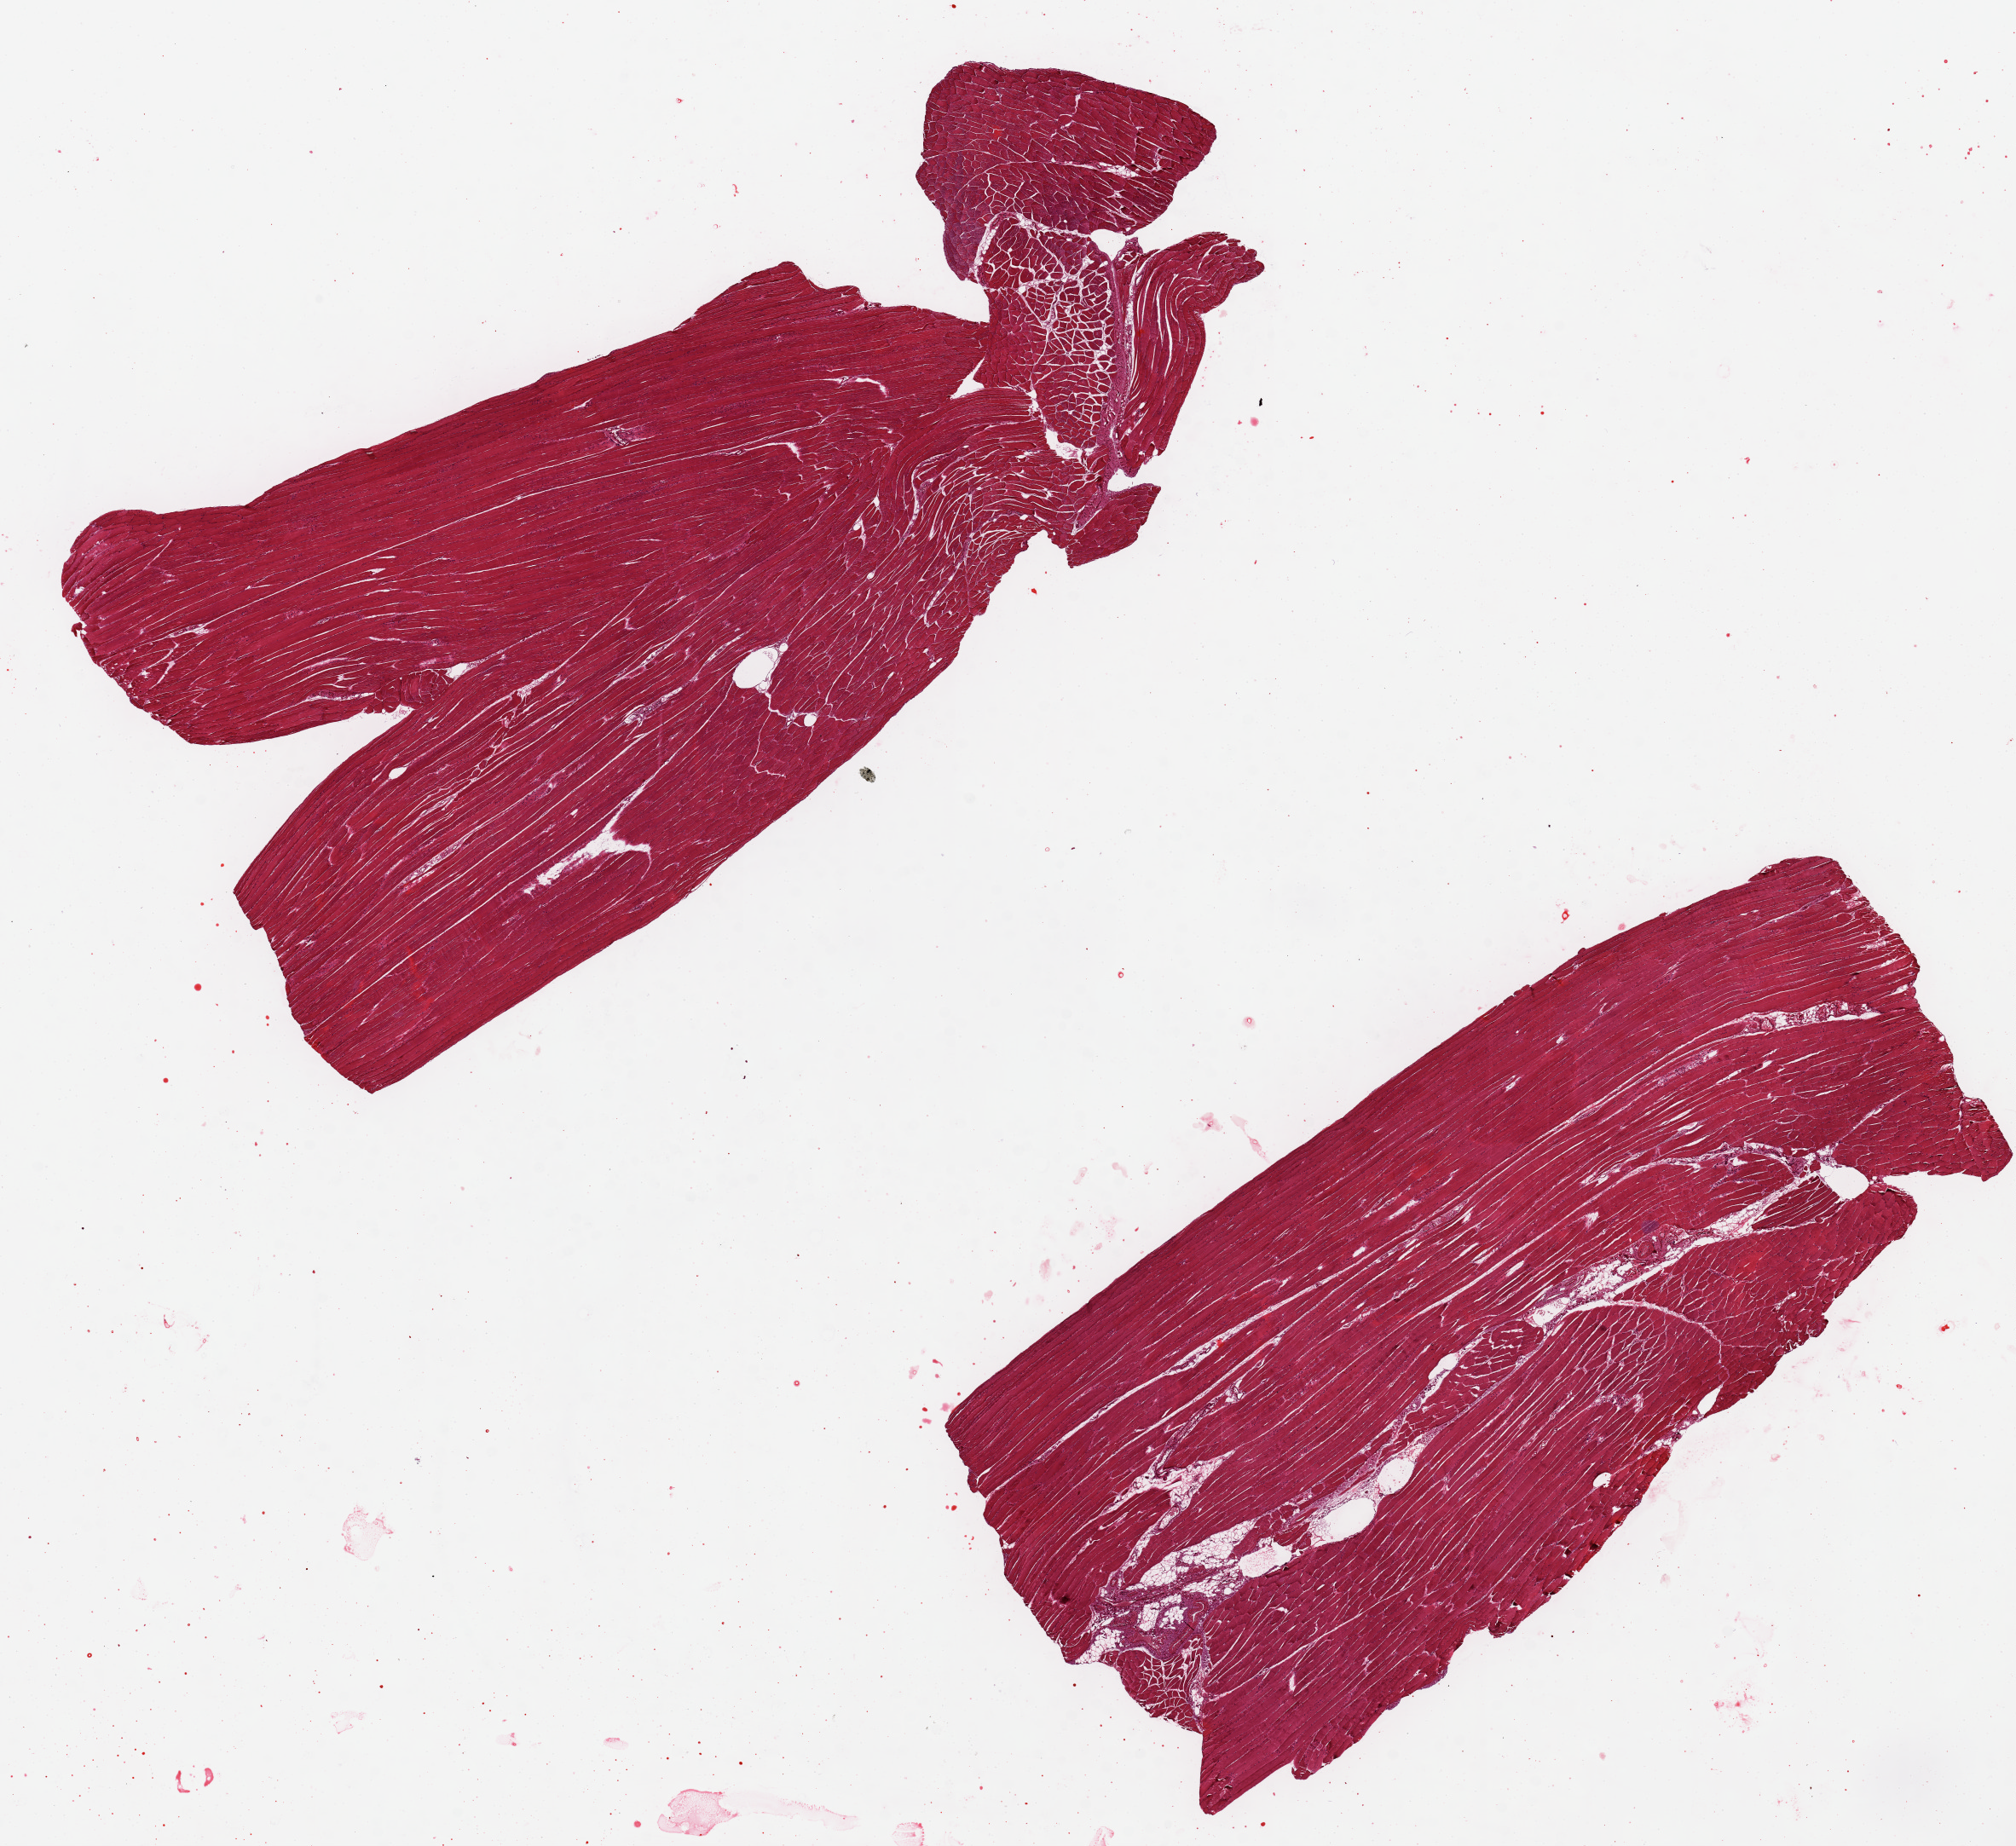
H&E whole-slide image — shown as a low-resolution overview of the whole scanned area (about 18.7 x 17.1 mm), PAXgene-fixed, paraffin-embedded tissue, target tissue: skeletal muscle, donor tissue sample.
* review note (as recorded): 2 pieces, 10x5 & 11x5